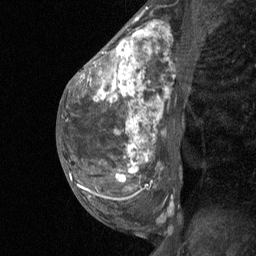
Breast MRI (dynamic contrast-enhanced), one sagittal slice. Position 31 of 64 along the scan axis. Dynamic contrast-enhanced study with each time point stored as its own series, time point 2 of 3 at this slice position (early post-contrast, ordered by acquisition time). 1.5 T. TE 4.8 ms, TR 27 ms. 256 × 256 image matrix, field of view 180 × 180 mm. Female patient, age 36 years. Case-level facts recorded for this patient, not image findings: setting: breast cancer imaged before/during neoadjuvant chemotherapy; receptor status: HR-positive, HER2-negative.
Outlined on this slice (semi-automatic segmentation, software-assisted and operator-edited):
- analysis volume of interest (the breast-tissue region the enhancement analysis was run in; not a lesion): box from (x=67, y=12) to (x=185, y=238) px
- tumour enhancement mask (voxels above the 90 % enhancement threshold inside the analysis volume of interest): (x=81, y=28)–(x=153, y=188)